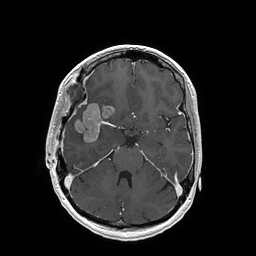
Brain MRI from a brain-tumour surgery series, one axial slice; position 110 of 202 along the scan axis; T1-weighted post-contrast; 256 × 256 image matrix, field of view 250 × 250 mm. From the clinical record (not read from this slice): histopathology: Glioblastoma; WHO grade: 4; IDH mutation: no; tumour location: Right Insular.
Annotated regions visible in this slice (manually delineated by an expert):
- tumour: bounding box [x1, y1, x2, y2] px = [74, 103, 115, 143]